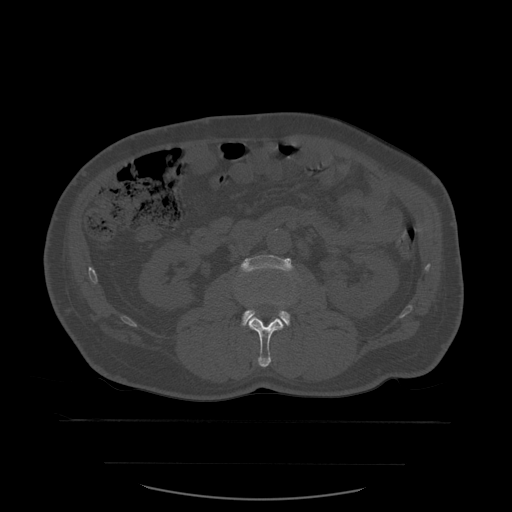
CT including the spine, one axial slice. Slice 208 of 590 in the series (ordered by position). Bone window (W 1800 / L 400 HU). 1.25 mm slice thickness. 512 × 512 image matrix, field of view 479 × 479 mm. Patient age 71 years. From the clinical record (not read from this slice): primary cancer: lung.
Structures marked on this image (semi-automatic segmentation, software-assisted and operator-edited):
- L2 vertebra: bounding box <245,295,291,368> (left, top, right, bottom; pixels)
- L3 vertebra: <239,255,294,326>